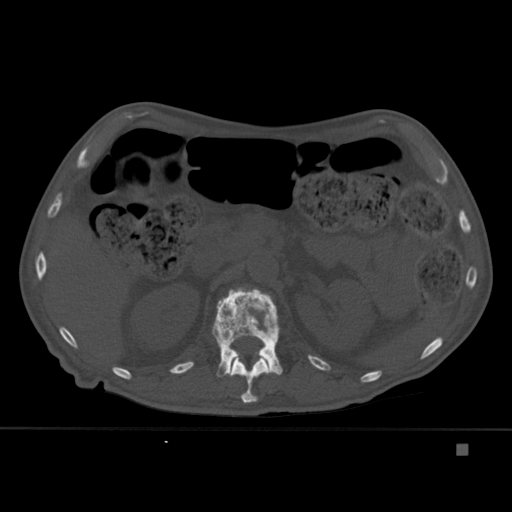
CT including the spine, one axial slice; position 189 of 451 along the scan axis; bone window (W 1800 / L 400 HU); 512 × 512 image matrix. Patient: male, 75 years. Case-level facts recorded for this patient, not image findings: primary cancer: prostate.
Structures marked on this image (semi-automatically segmented with operator editing):
- L1 vertebra: bounding box <212,288,283,377> (left, top, right, bottom; pixels)
- T12 vertebra: <230,353,271,403>